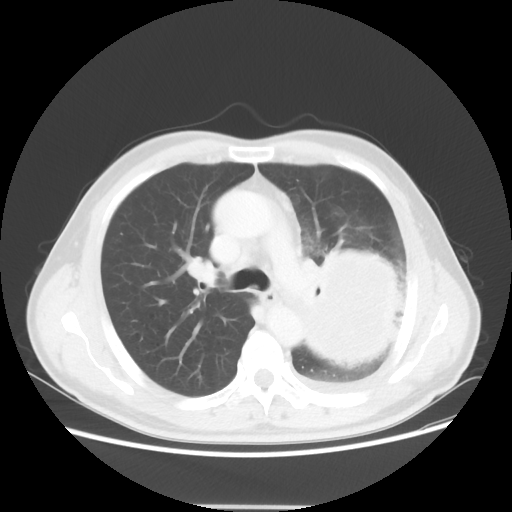
Chest CT, one axial slice. Slice 35 of 53 in the series (ordered by position). 100 kVp. Lung window (W 1500 / L -600 HU). 512 × 512 image matrix, field of view 391 × 391 mm. Patient: male, 60 years. From the clinical record (not read from this slice): clinical TNM (as recorded): T4 N1 M1a; histopathological grade: G3.
Structures marked on this image (bounding box drawn by a radiologist):
- lung tumour (recorded histology: large cell carcinoma): bounding box <307,252,413,366> (left, top, right, bottom; pixels)